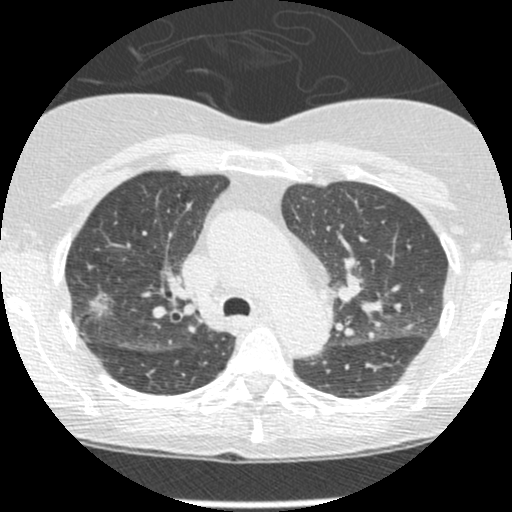
Low-dose screening chest CT, one axial slice. Slice 173 of 238 in the series (ordered by position). Reconstruction kernel STANDARD. Lung window (W 1500 / L -600 HU). 1.25 mm slice thickness. 512 × 512 image matrix, field of view 288 × 288 mm.
Structures marked on this image (outlined manually by an expert reader):
- lesion 1 (tumor, upper lobe of right lung): bounding box (x1, y1, x2, y2) in pixels: (90, 294, 109, 315)